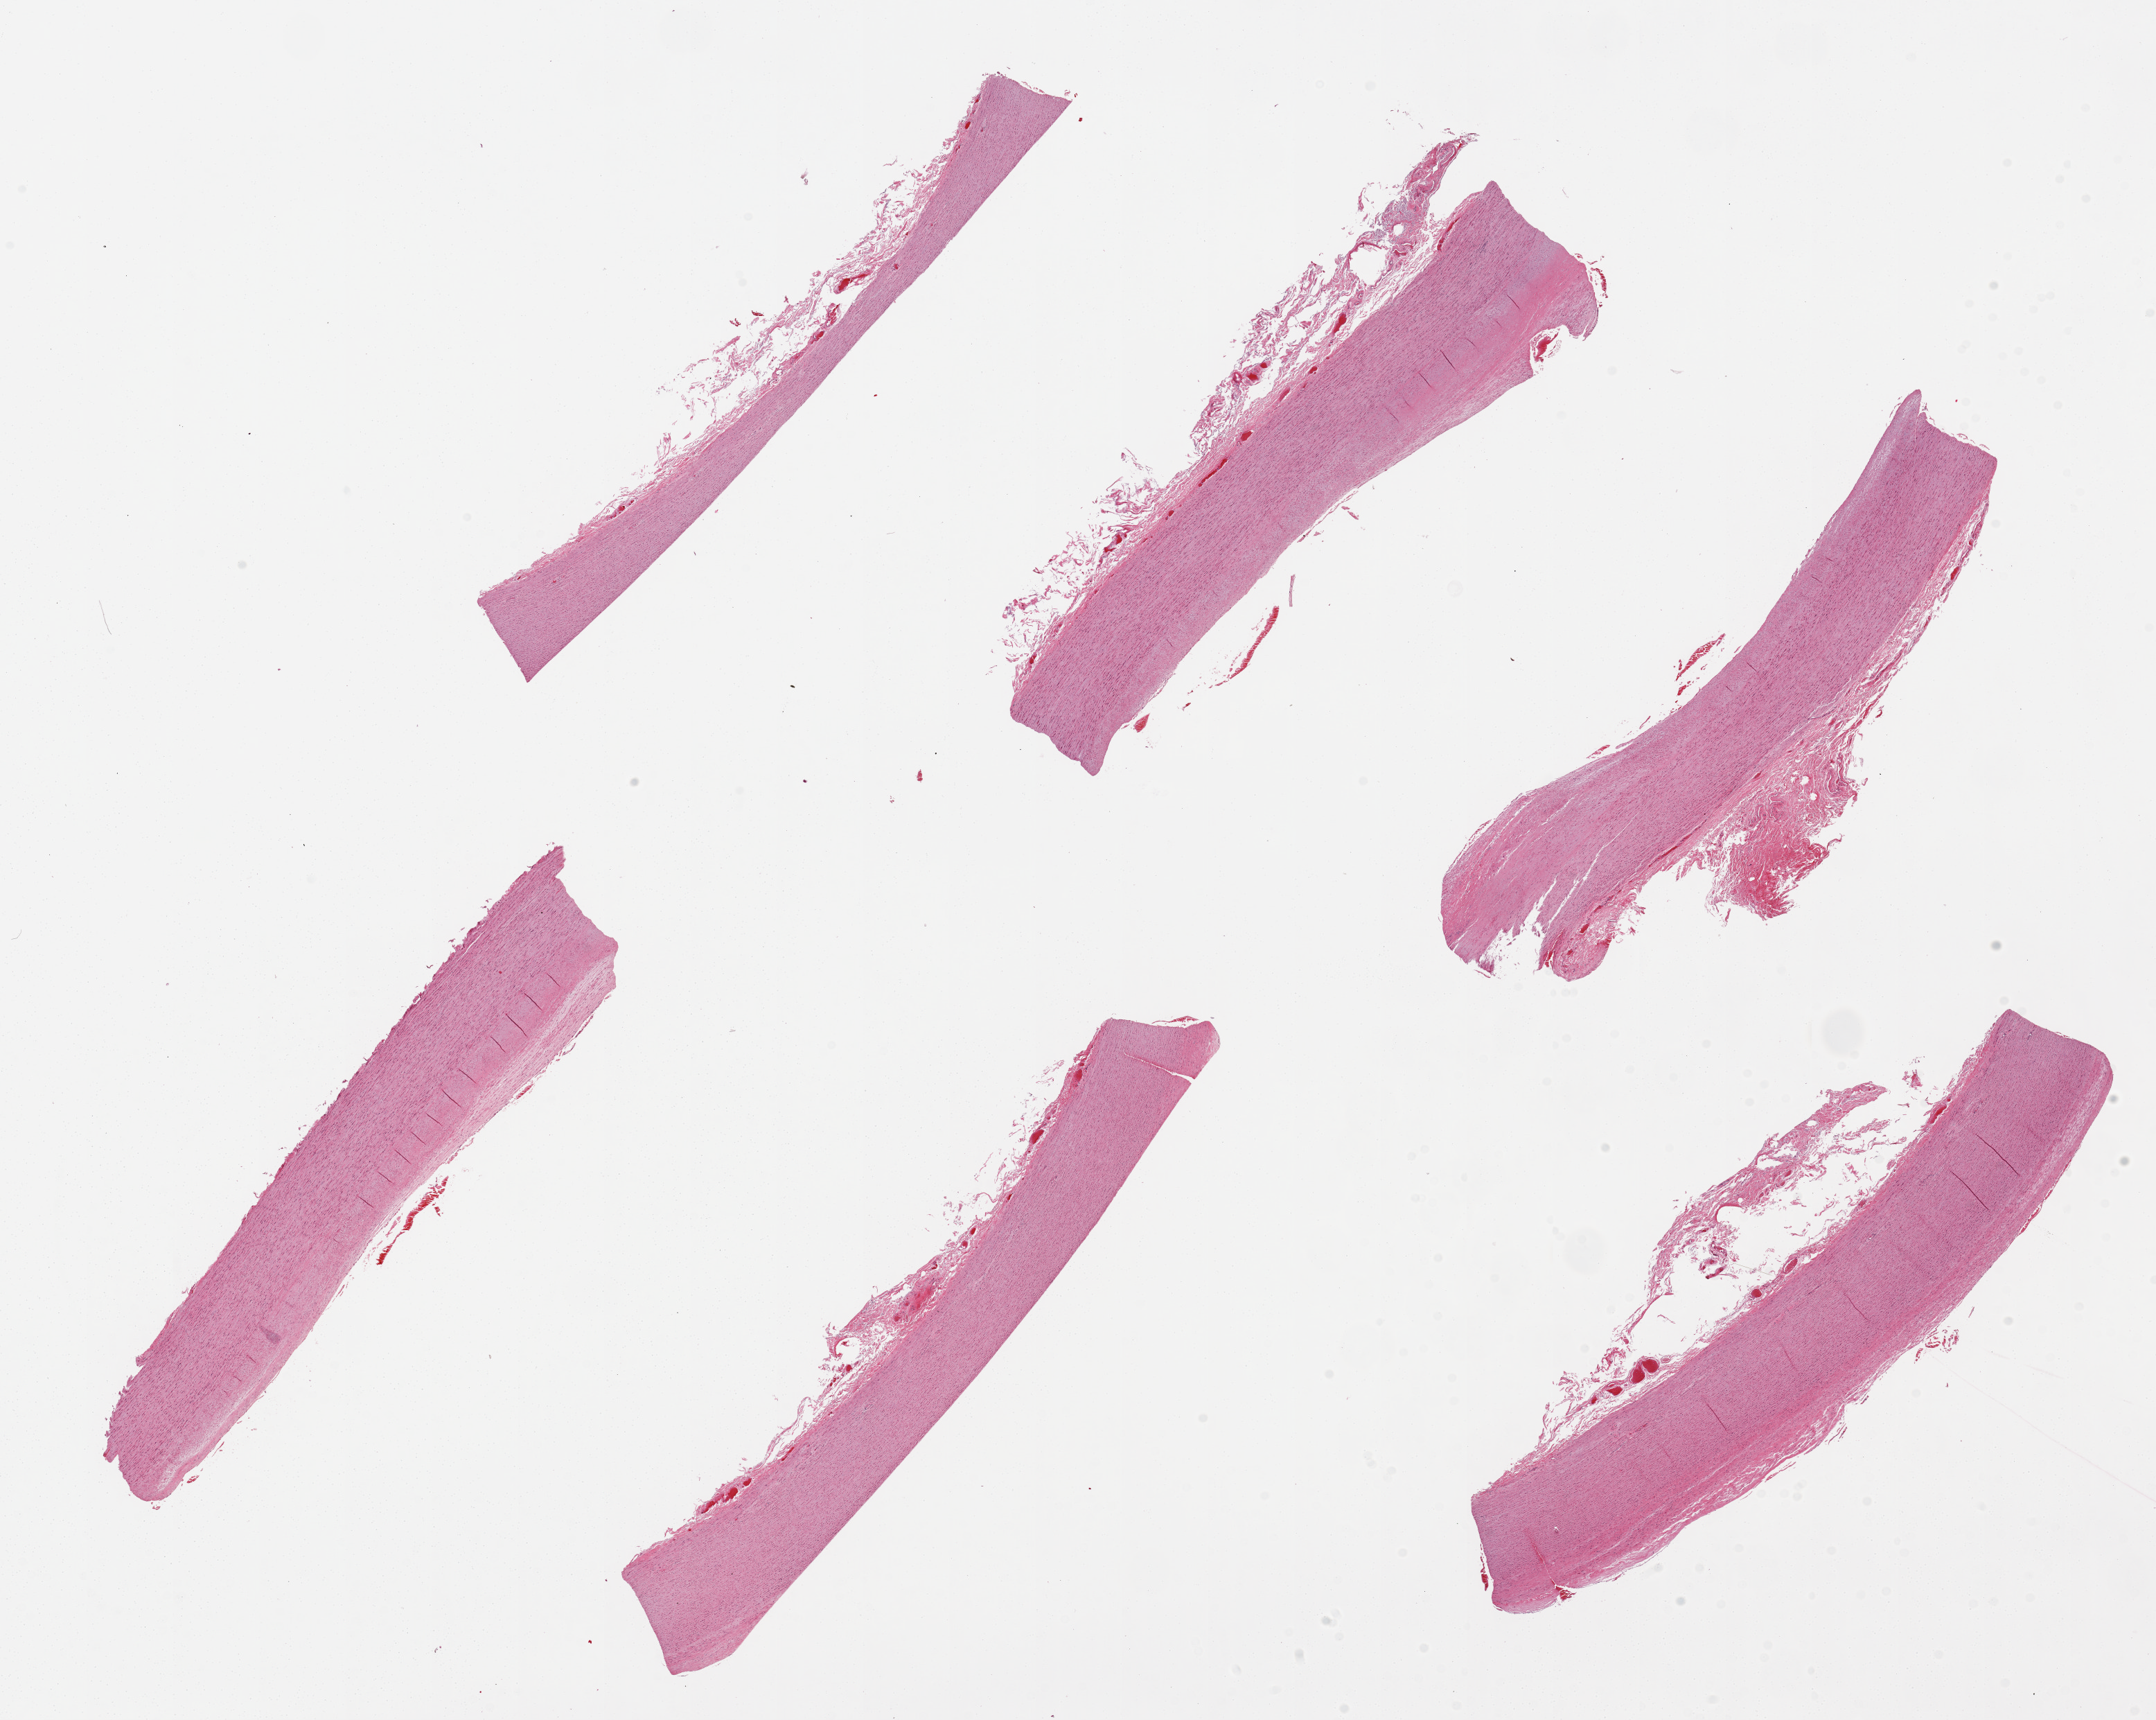
Digitized haematoxylin and eosin-stained section, shown as a low-resolution overview of the whole scanned area (about 24.6 x 19.6 mm, acquisition: 20x scan); PAXgene-fixed, paraffin-embedded tissue; section of aorta (target tissue); donor tissue sample. Male donor.
Reviewer comment on this tissue sample: 6 pieces; atherosclerosis.